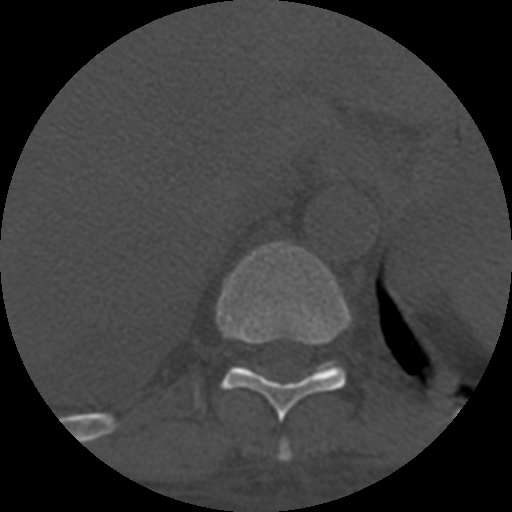
CT including the spine, one axial slice; reconstruction kernel STANDARD; one of 3 acquisitions stored at this slice position; bone window (W 1800 / L 400 HU); 1.25 mm slice thickness; 512 × 512 image matrix, field of view 160 × 160 mm. Patient age 55 years. Case-level facts recorded for this patient, not image findings: primary cancer: colon; vertebrae with lytic lesions (as recorded): T12, L1, L5.
Outlined on this slice (semi-automatically segmented with operator editing):
- T10 vertebra: bounding box <216,241,350,421> (left, top, right, bottom; pixels)
- T11 vertebra: <313,362,342,375>
- T9 vertebra: <278,440,292,462>